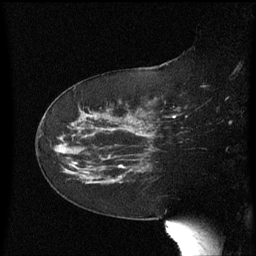
Breast MRI (dynamic contrast-enhanced), one sagittal slice. Position 36 of 60 along the scan axis. Dynamic contrast-enhanced series, image 2 of 3 at this slice position (ordered by acquisition). 1.5 T. TE 4.2 ms, TR 8.4 ms. 2.3 mm slice thickness. 256 × 256 image matrix. Patient: female, 63 years. From the clinical record (not read from this slice): setting: breast cancer imaged before/during neoadjuvant chemotherapy; receptor status: HER2-positive.
Outlined on this slice (semi-automatically segmented with operator editing):
- analysis volume of interest (the breast-tissue region the enhancement analysis was run in; not a lesion): bounding box <66,136,138,185> (left, top, right, bottom; pixels)
- tumour enhancement mask (voxels above the 70 % enhancement threshold inside the analysis volume of interest): <119,166,124,169>